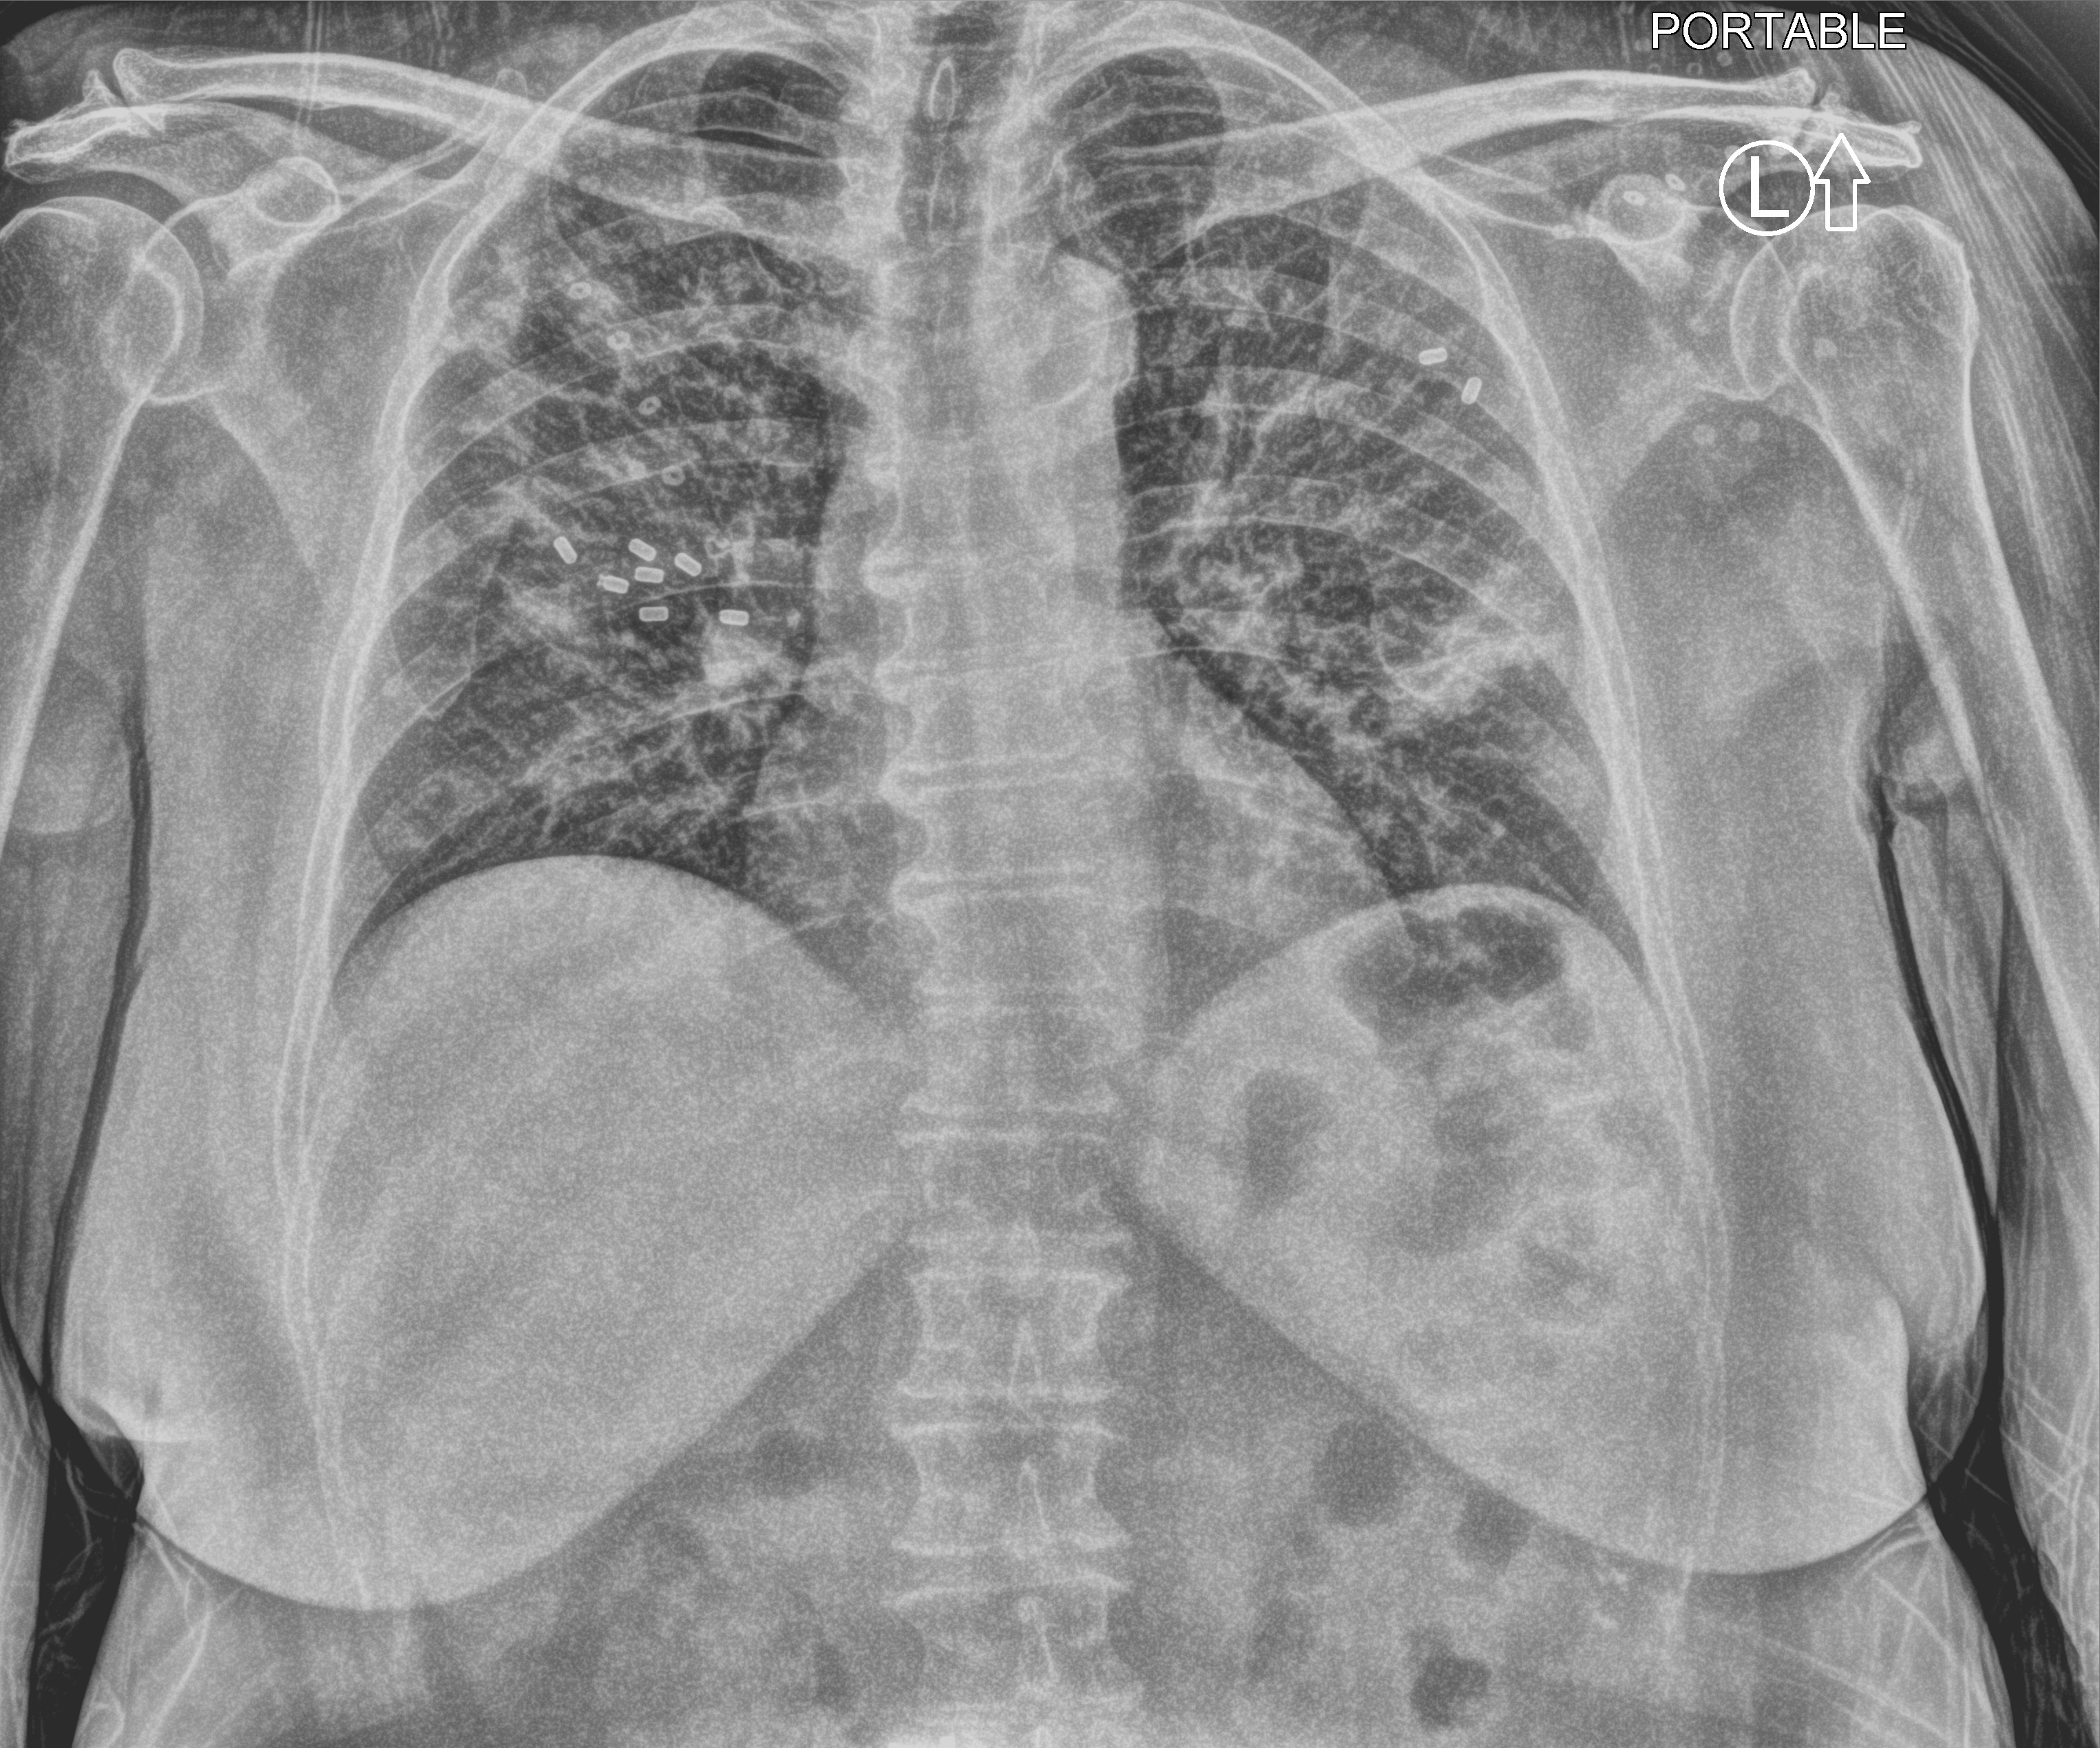
Chest X-ray (portable), anteroposterior (AP) projection. Female patient hospitalised with COVID-19, age 60–74 years.
From the hospital-stay record, not from the radiograph (when in the stay this image was taken is not recorded): chronic kidney disease (admission record): no; mechanically ventilated during this hospital stay: no.